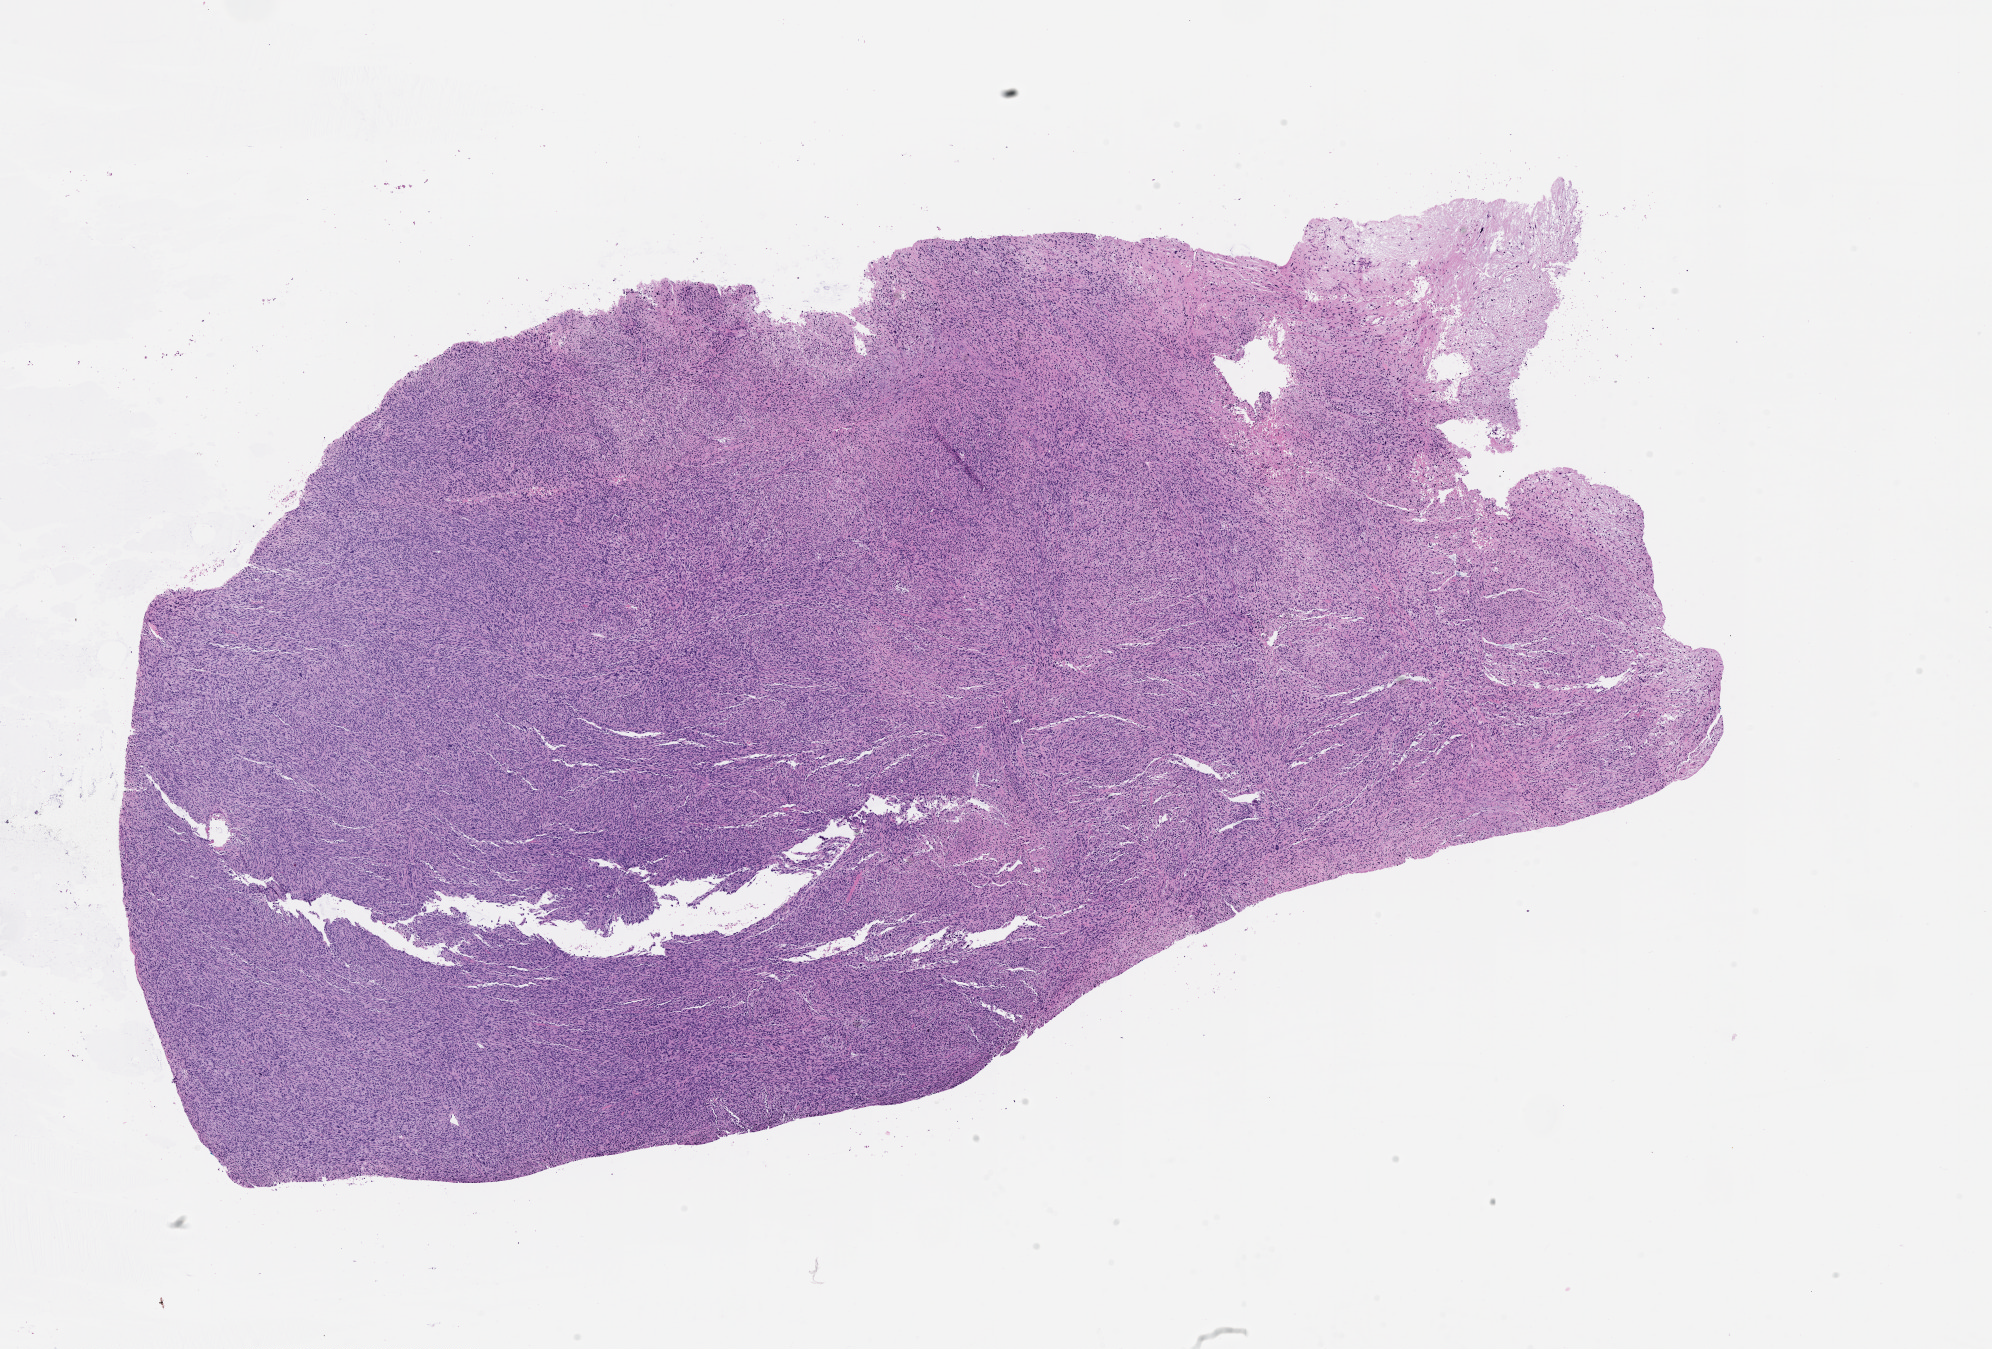
Whole-slide histology image, Hematoxylin and eosin (H&E) stained — shown as a low-resolution overview of the whole scanned area (about 16.0 x 10.9 mm, acquisition: 20x scan).
Patient diagnosis (cohort enrolment): sarcoma (site not recorded at cohort level).